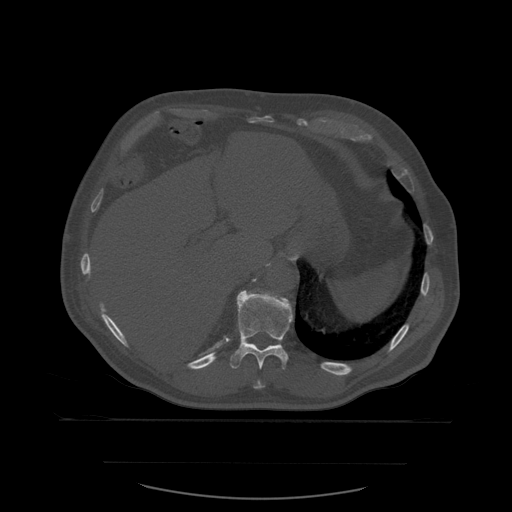
CT including the spine, one axial slice. Bone window (W 1800 / L 400 HU). 1.25 mm slice thickness. 512 × 512 image matrix. Patient age 71 years. Case-level facts recorded for this patient, not image findings: primary cancer: lung; vertebrae with lytic lesions (as recorded): T1, T2, L5, S1.
Structures marked on this image (semi-automatic segmentation, software-assisted and operator-edited):
- T10 vertebra: bounding box [x1, y1, x2, y2] px = [254, 380, 265, 389]
- T11 vertebra: [230, 290, 294, 389]
- T12 vertebra: [267, 292, 274, 296]